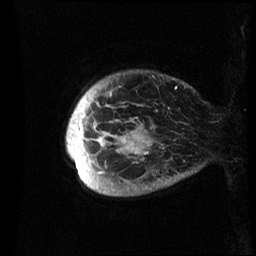
Breast MRI (dynamic contrast-enhanced), one sagittal slice. Slice 2 of 60 in the series (ordered by position). Dynamic contrast-enhanced series, image 2 of 3 at this slice position (ordered by acquisition). 1.5 T. TE 4.2 ms, TR 8.4 ms. 2.4 mm slice thickness. 256 × 256 image matrix. Female patient, age 48 years.
Annotated regions visible in this slice (semi-automatically segmented with operator editing):
- analysis volume of interest (the breast-tissue region the enhancement analysis was run in; not a lesion): bounding box [x1, y1, x2, y2] px = [66, 77, 189, 195]
- tumour enhancement mask (voxels above the 70 % enhancement threshold inside the analysis volume of interest): [66, 92, 148, 179]